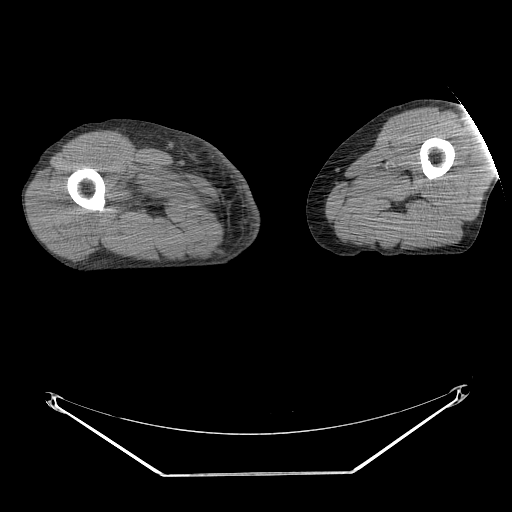
CT of an extremity soft-tissue mass (from a PET/CT study), one axial slice. Position 231 of 311 along the scan axis. Reconstruction kernel STANDARD. Soft-tissue window (W 400 / L 40 HU). 3.75 mm slice thickness. 512 × 512 image matrix, field of view 500 × 500 mm. Male patient. From the clinical record (not read from this slice): histological type: undifferentiated - pleiomorphic; grade: high; site of the primary tumour: right thigh.
Structures marked on this image (expert contour drawn on MRI and transferred to this co-registered scan by the dataset authors):
- gross tumour volume including surrounding oedema: bounding box <146,199,159,213> (left, top, right, bottom; pixels)